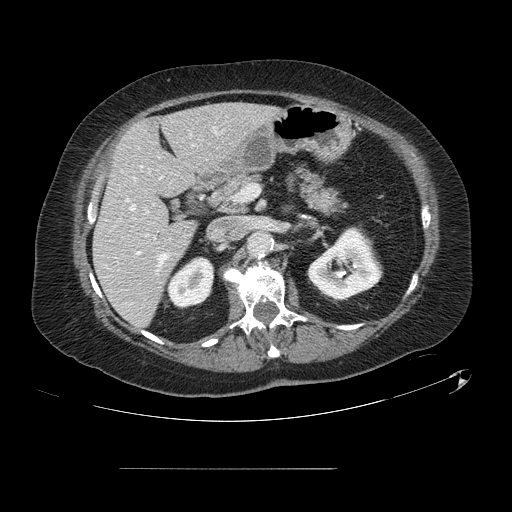
Contrast-enhanced abdominal CT, one axial slice; position 62 of 148 along the scan axis; soft-tissue window (W 400 / L 40 HU); 2.5 mm slice thickness; 512 × 512 image matrix, field of view 439 × 439 mm. Female patient, age 75 years. From the clinical record (not read from this slice): diagnosis: colorectal cancer liver metastases, imaged before liver resection; multiple liver metastases: no; largest metastasis: 2.4 cm.
Annotated regions visible in this slice (outlined manually by an expert reader):
- hepatic veins: bounding box (x1, y1, x2, y2) in pixels: (127, 132, 217, 267)
- liver: (94, 105, 276, 328)
- planned liver remnant (the part of the liver to remain after resection): (94, 104, 277, 328)
- portal vein (with intrahepatic branches): (136, 211, 148, 255)